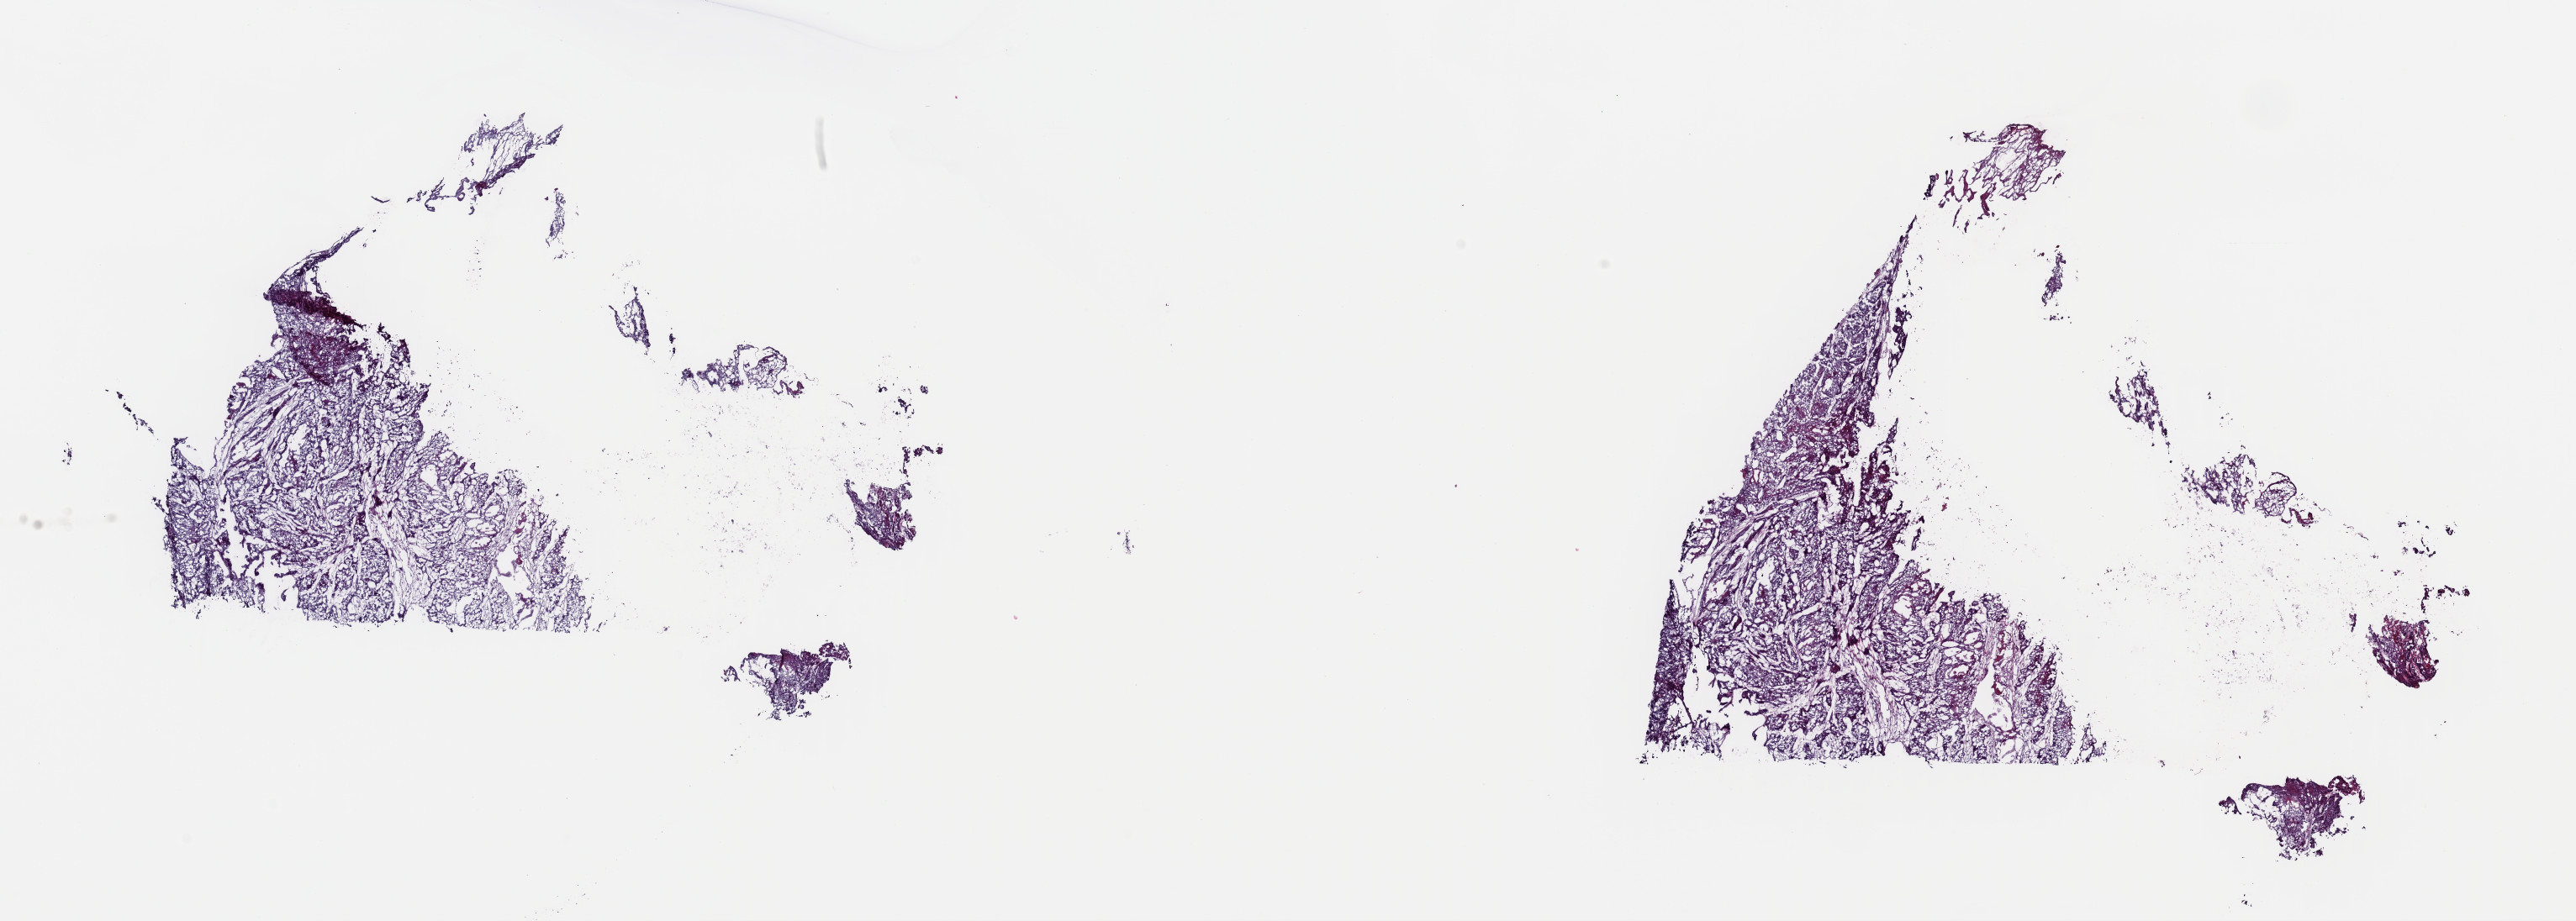
Whole-slide histology image, H&E-stained — a low-resolution overview of the entire scanned area, about 24.2 x 8.7 mm (from a 40x scan), frozen section from the top of the tissue portion, sample: primary tumour, bladder. Male, age 66 years at initial diagnosis. Histologic grade: high grade. Pathologist review of this section (percent, as recorded): tumour cells 80%, tumour nuclei 80%, normal cells 0%, stromal cells 20%, necrosis 0%. Infiltration values recorded for this section: lymphocyte infiltration 2%, monocyte infiltration 1%, neutrophil infiltration 1%.
AJCC pathologic stage: II (6th edition). Diagnosis: Transitional cell carcinoma. TNM: NX MX.